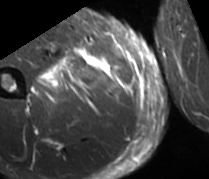
MRI of an extremity soft-tissue mass, one axial slice; slice 26 of 89 in the series (ordered by position); STIR; MR volume resampled by the dataset authors to the PET/CT grid (not the native acquisition matrix); 3.27 mm slice thickness; 209 × 179 image matrix. Male patient. From the clinical record (not read from this slice): histological type: undifferentiated - pleiomorphic; grade: high; site of the primary tumour: right thigh.
Outlined on this slice (expert contour drawn on MRI and transferred to this co-registered scan by the dataset authors):
- gross tumour volume including surrounding oedema: bounding box <32,51,109,101> (left, top, right, bottom; pixels)